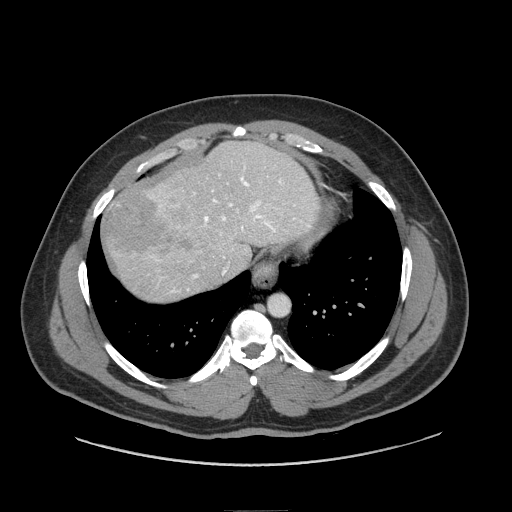
Contrast-enhanced abdominal CT (liver protocol), one axial slice; position 67 of 87 along the scan axis; 140 kVp; soft-tissue window (W 400 / L 40 HU); 512 × 512 image matrix. Case-level facts recorded for this patient, not image findings: diagnosis: hepatocellular carcinoma (patient treated with transarterial chemoembolisation; whether this scan precedes or follows treatment is not stated here); TNM stage (as recorded): Stage-II; Child-Pugh class: A; tumour differentiation: moderately differentiated.
Structures marked on this image (semi-automatically segmented with operator editing):
- liver parenchyma outside the tumour (the mass and vessels are separate outlines, so this box may not span the whole liver): bounding box <102,142,318,302> (left, top, right, bottom; pixels)
- mass: <102,179,198,262>
- liver vessels: <171,166,309,293>